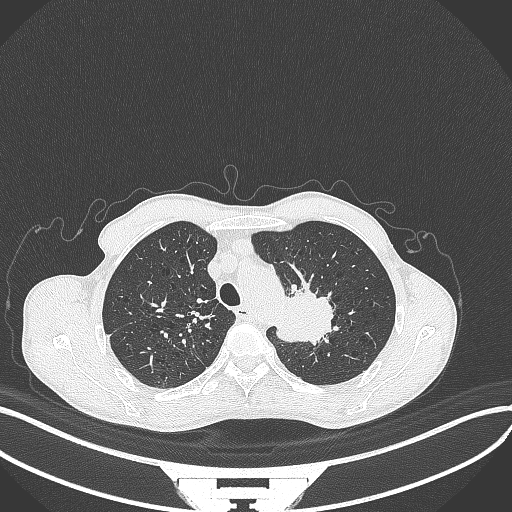
Chest CT, one axial slice. Position 333 of 386 along the scan axis. Reconstruction kernel B70f. 120 kVp. Lung window (W 1500 / L -600 HU). 1 mm slice thickness. 512 × 512 image matrix, field of view 400 × 400 mm. Patient: male, 65 years. Case-level facts recorded for this patient, not image findings: clinical TNM (as recorded): T2b N0 M0; histopathological grade: G2.
Outlined on this slice (rectangle marked by the reading radiologist):
- lung tumour (recorded histology: adenocarcinoma): bounding box (x1, y1, x2, y2) in pixels: (269, 286, 341, 345)